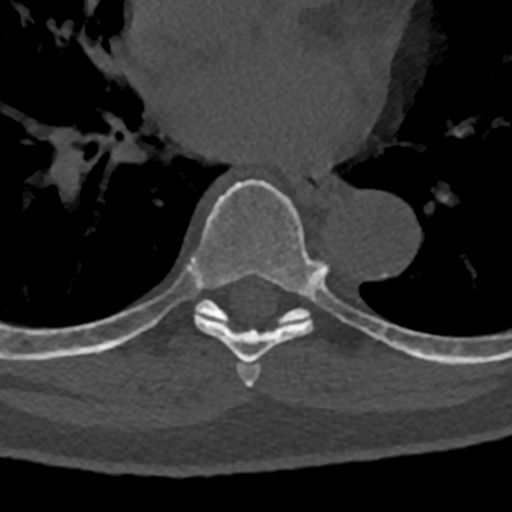
CT including the spine, one axial slice. Slice 749 of 797 in the series (ordered by position). 120 kVp. Bone window (W 1800 / L 400 HU). 512 × 512 image matrix, field of view 160 × 160 mm. Male patient, age 74 years. From the clinical record (not read from this slice): primary cancer: renal; vertebrae with lytic lesions (as recorded): T10, L1, L2, L3, L4, L5.
Outlined on this slice (semi-automatically segmented with operator editing):
- T6 vertebra: bounding box [x1, y1, x2, y2] px = [237, 363, 261, 388]
- T7 vertebra: [71, 179, 381, 365]
- T8 vertebra: [70, 300, 432, 362]